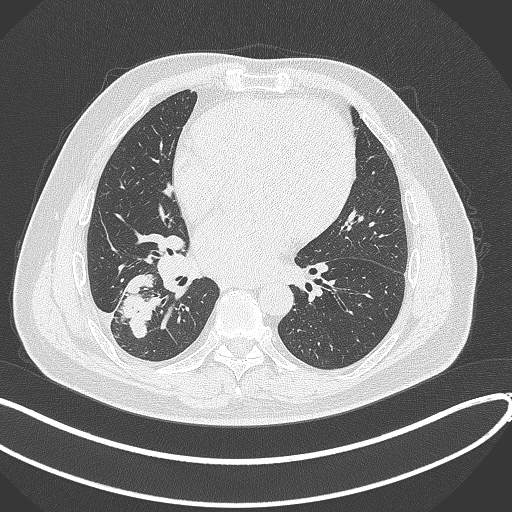
Chest CT, one axial slice. Slice 162 of 360 in the series (ordered by position). Reconstruction kernel B70f. 120 kVp. Lung window (W 1500 / L -600 HU). 512 × 512 image matrix. Male patient, age 59 years.
Annotated regions visible in this slice (bounding box drawn by a radiologist):
- lung tumour (recorded histology: adenocarcinoma): bounding box (x1, y1, x2, y2) in pixels: (121, 272, 165, 339)